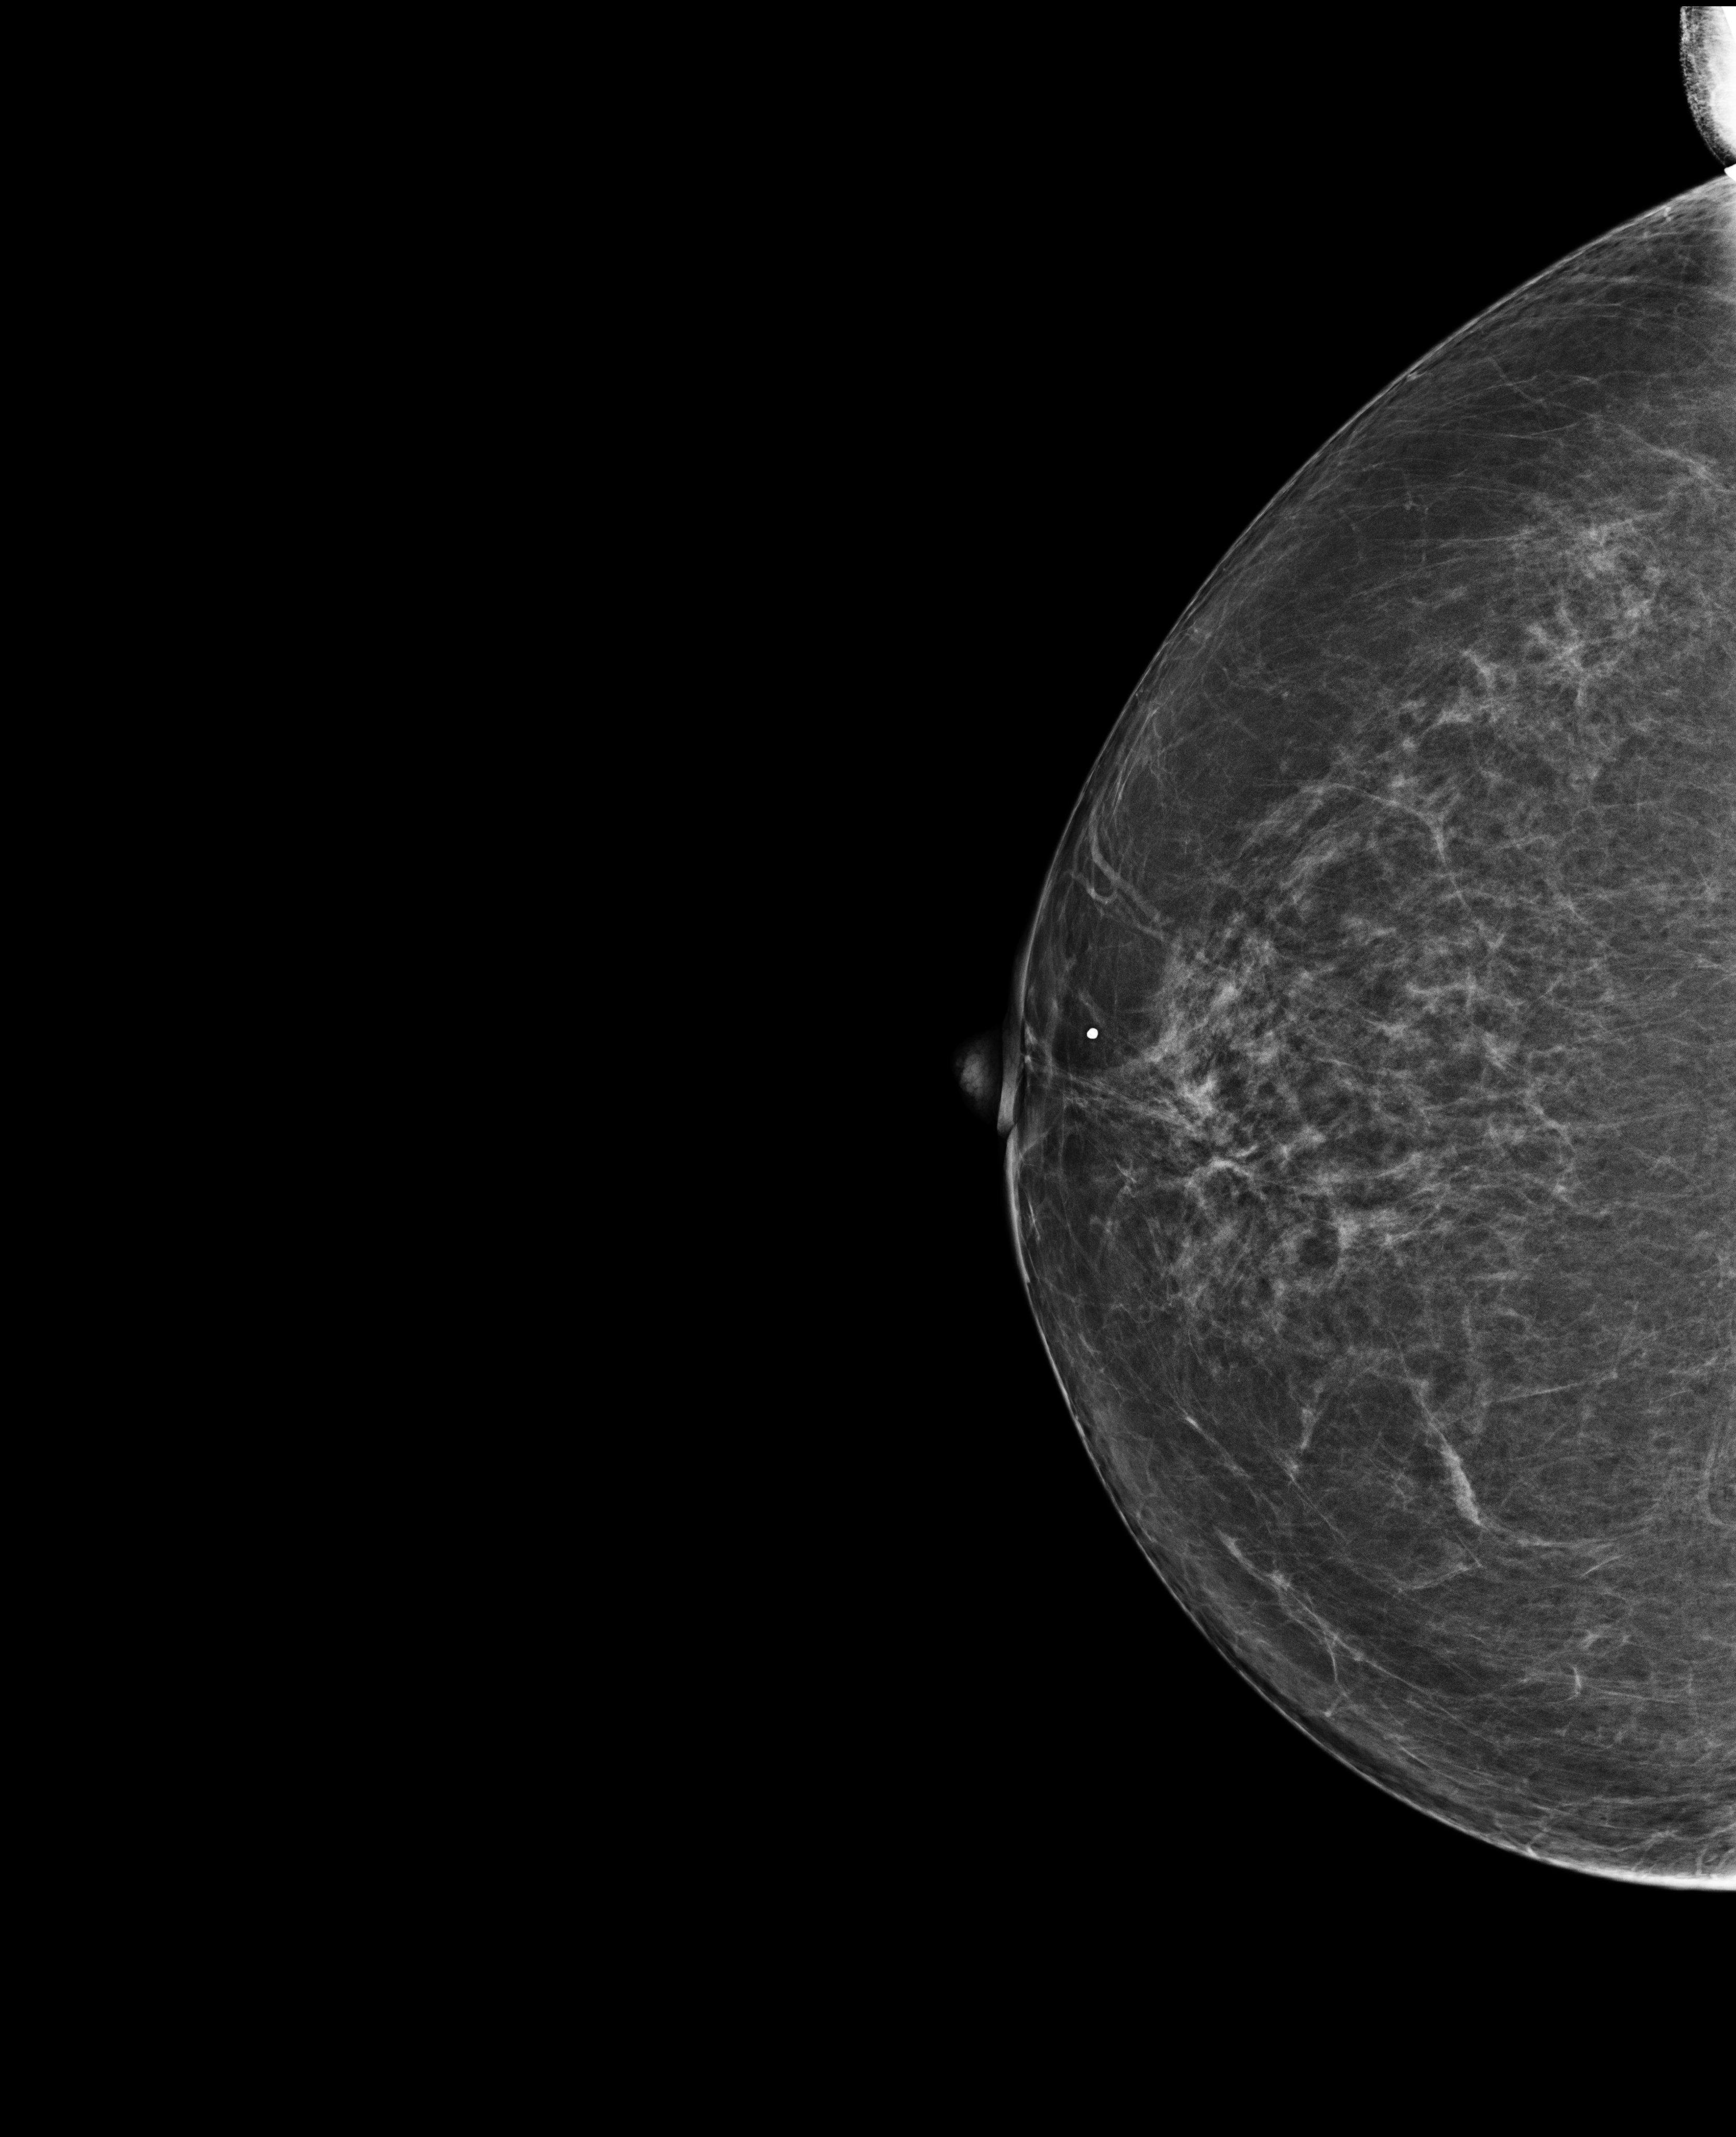
Full-field digital mammogram (FFDM); right breast; CC view; annual screening mammography examination; compressed breast thickness 70 mm; system: Selenia Dimensions. Patient: female, 74 years.
BI-RADS breast density category at the screening exam (both breasts, scale 1–4): 3. Final BI-RADS category for the screening round (tomosynthesis exam, both breasts): category 4. Recall: recalled for additional imaging after this screen.